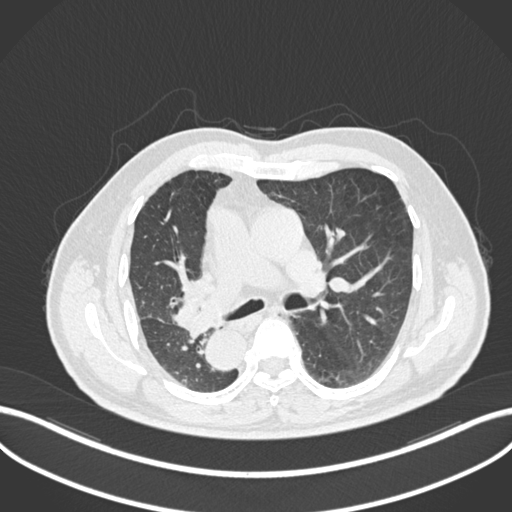
Chest CT, one axial slice. Slice 134 of 206 in the series (ordered by position). Lung window (W 1500 / L -600 HU). 1 mm slice thickness. 512 × 512 image matrix, field of view 400 × 400 mm. Patient: male, 67 years. From the clinical record (not read from this slice): clinical TNM (as recorded): T2a N0 M0.
Annotated regions visible in this slice (bounding box drawn by a radiologist):
- lung tumour (recorded histology: squamous cell carcinoma): bounding box <161,274,207,324> (left, top, right, bottom; pixels)